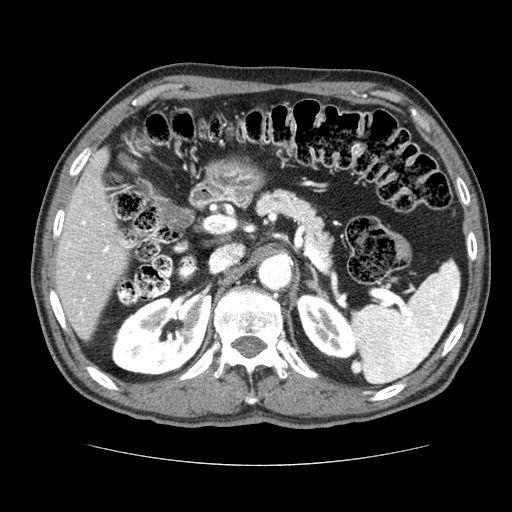
Contrast-enhanced abdominal CT (liver protocol), one axial slice; position 40 of 79 along the scan axis; 120 kVp; soft-tissue window (W 400 / L 40 HU); 2.5 mm slice thickness; 512 × 512 image matrix, field of view 360 × 360 mm. From the clinical record (not read from this slice): diagnosis: hepatocellular carcinoma (patient treated with transarterial chemoembolisation; whether this scan precedes or follows treatment is not stated here); TNM stage (as recorded): Stage-I; Child-Pugh class: A; tumour nodularity: uninodular.
Outlined on this slice (semi-automatic segmentation, software-assisted and operator-edited):
- liver parenchyma outside the tumour (the mass and vessels are separate outlines, so this box may not span the whole liver): bounding box [x1, y1, x2, y2] px = [54, 148, 128, 340]
- liver vessels: [64, 206, 127, 320]